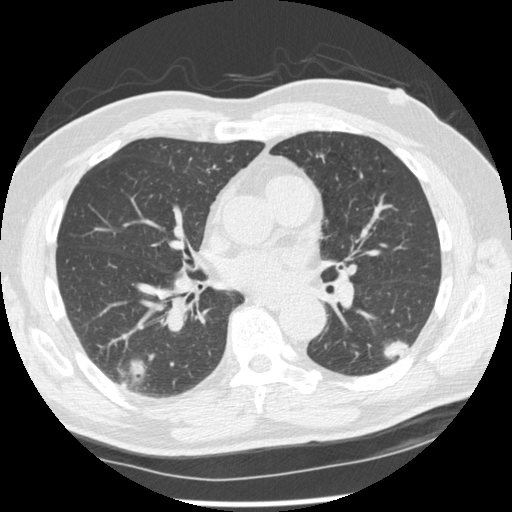
Axial slice from a low-dose chest CT screening exam; second screening round (one year after baseline); lung window (W 1500 / L -600 HU); 1.25 mm slice thickness; standard (soft-tissue) reconstruction kernel (STANDARD); slice 124 of 227 in the series; 512 × 512 image matrix, field of view 360 × 360 mm. Male participant, aged 74 years at enrolment. Former smoker at enrolment.
Lesion marked by an expert reader, bounding box <366,313,424,369> (left, top, right, bottom; pixels). The screening reader recorded 7 non-calcified nodules or masses ≥4 mm on this exam (right upper lobe, right lower lobe, right upper lobe, right lower lobe, left lower lobe, left upper lobe, left upper lobe); which of them this box marks is not recorded.